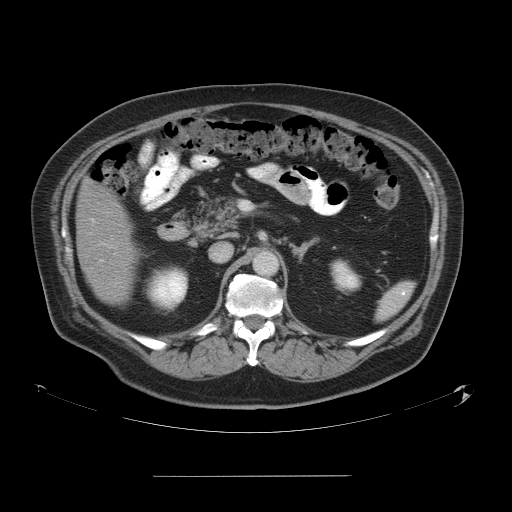
Contrast-enhanced abdominal CT, one axial slice. Intravenous contrast given. Soft-tissue window (W 400 / L 40 HU). 5 mm slice thickness. 512 × 512 image matrix, field of view 480 × 480 mm. Male patient, age 63 years. From the clinical record (not read from this slice): diagnosis: colorectal cancer liver metastases, imaged before liver resection; multiple liver metastases: no; largest metastasis: 4.2 cm; chemotherapy before resection: yes.
Structures marked on this image (manually delineated by an expert):
- liver: box from (x=76, y=182) to (x=131, y=303) px
- planned liver remnant (the part of the liver to remain after resection): (x=76, y=181)–(x=132, y=303)
- portal vein (with intrahepatic branches): (x=92, y=219)–(x=103, y=262)